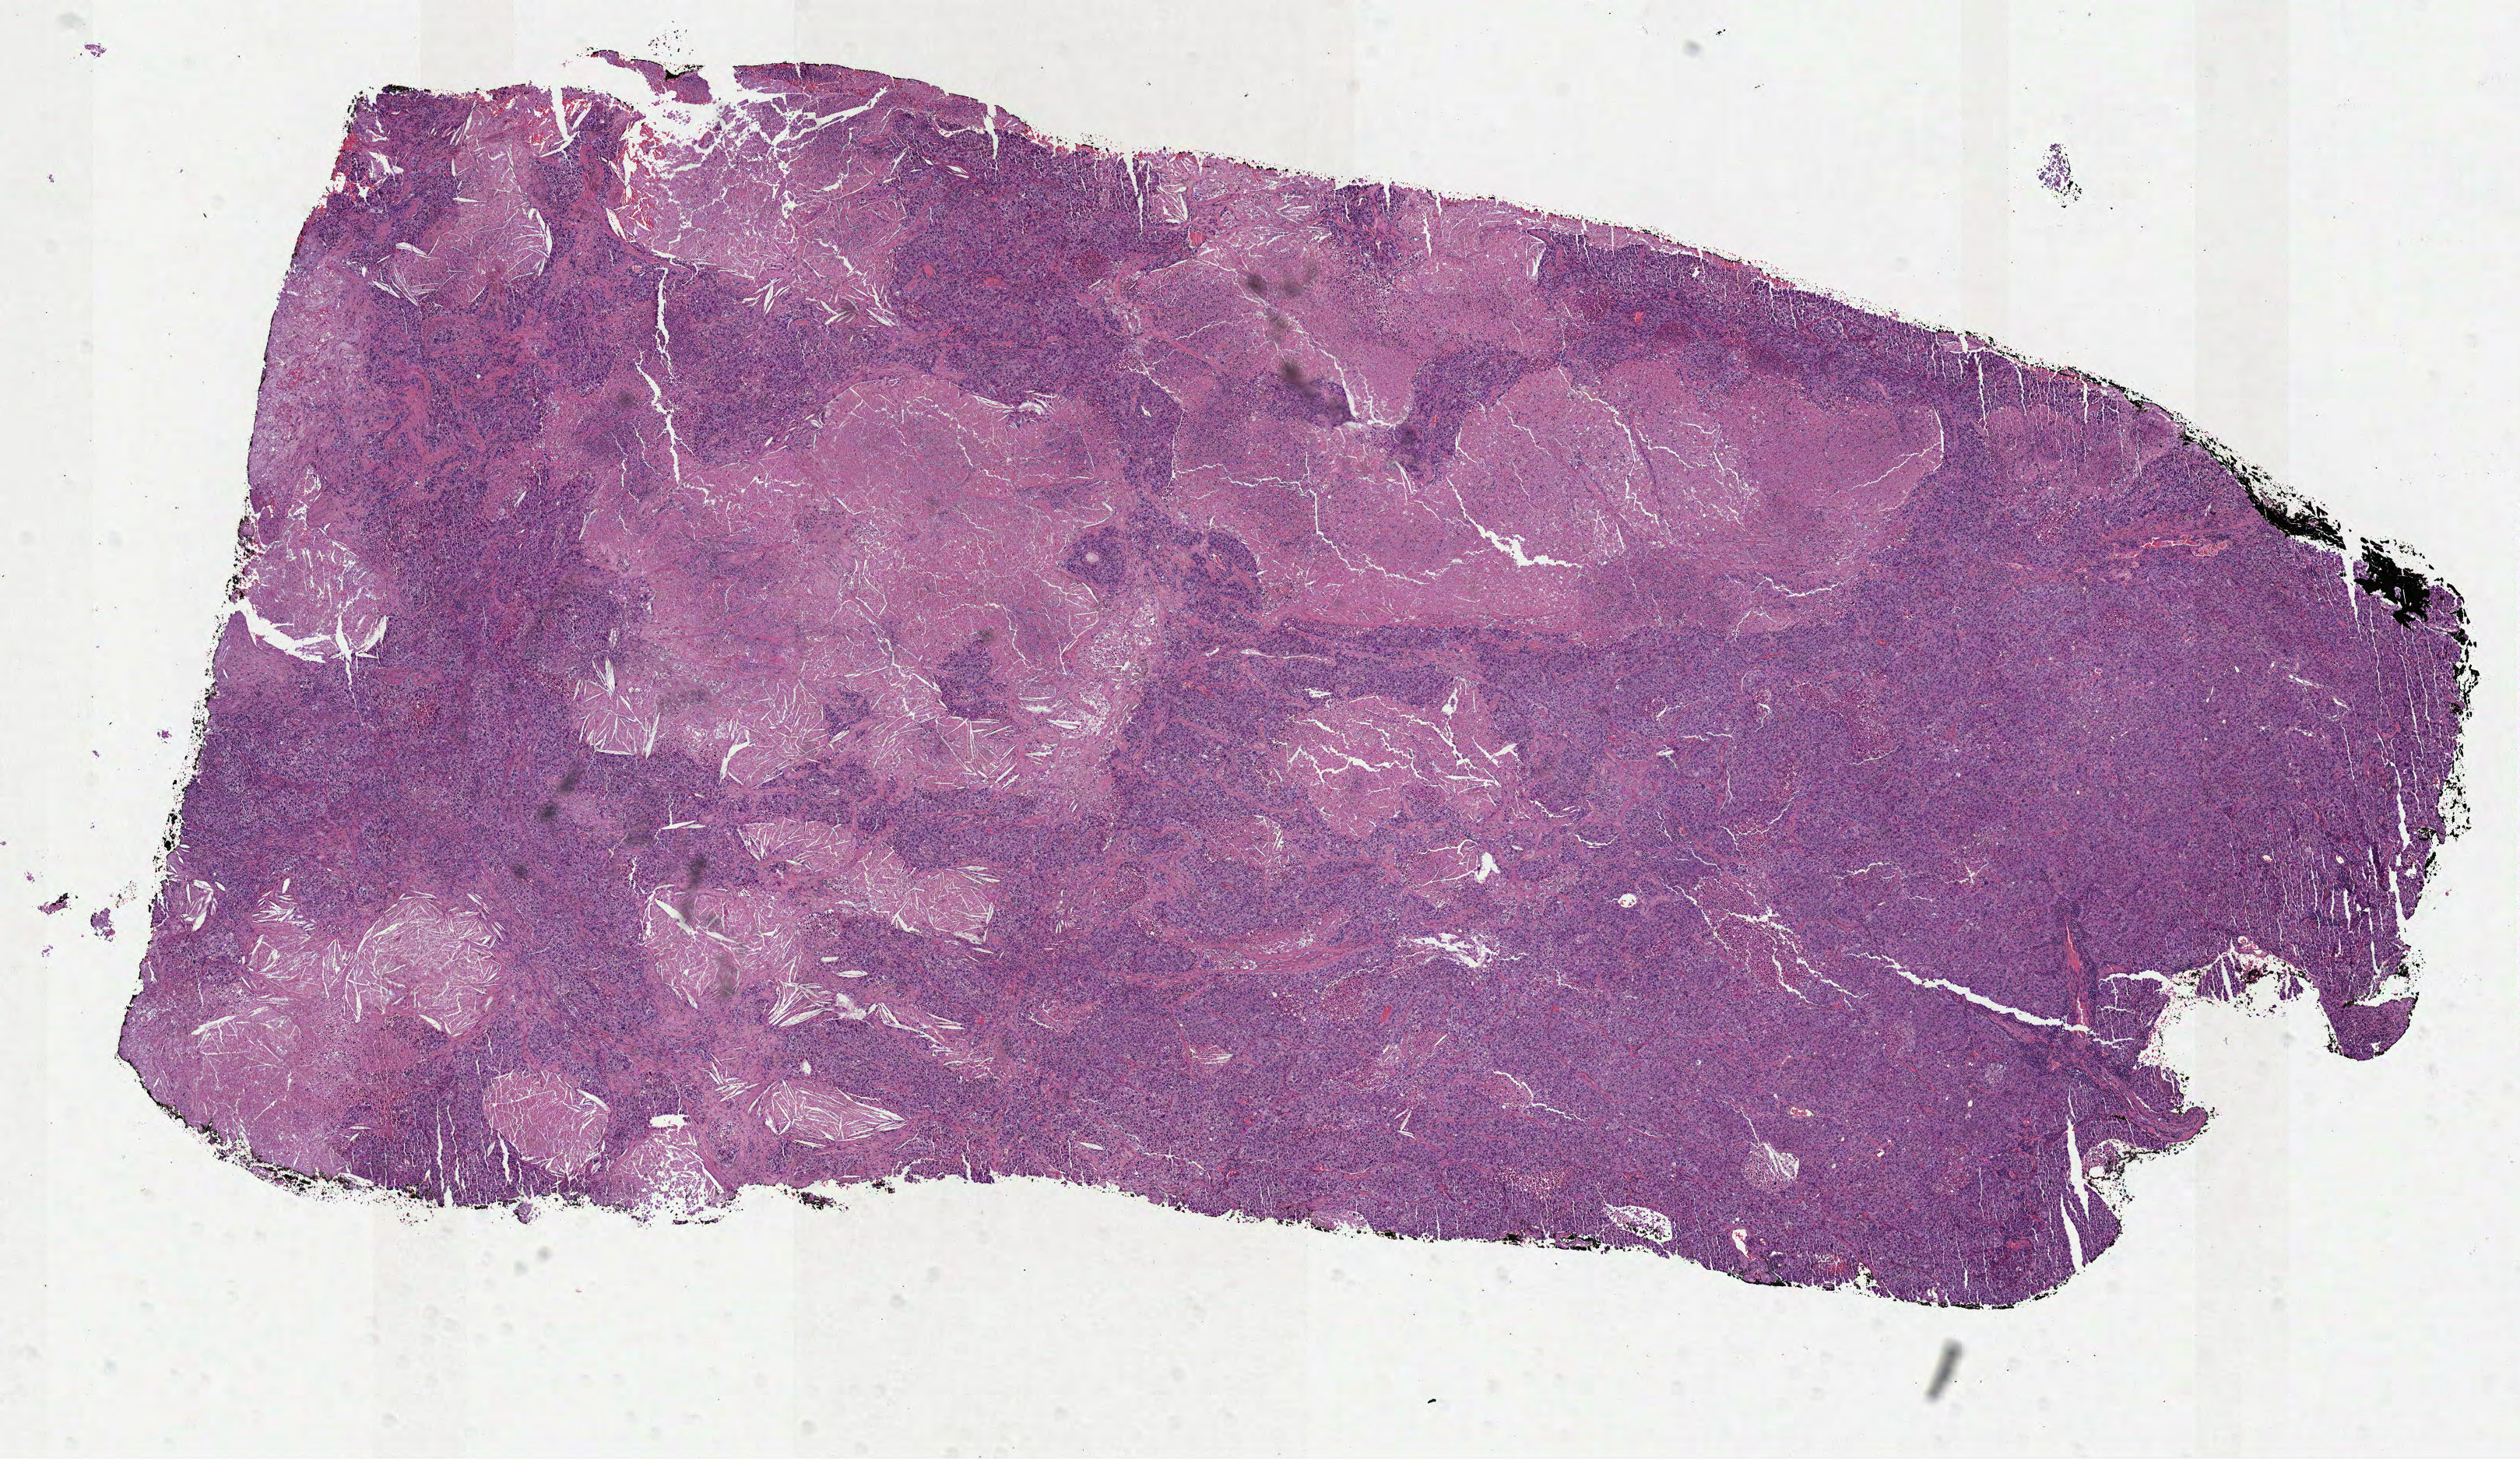
H&E whole-slide image — whole scanned area (about 13.1 x 7.6 mm) shown as a low-resolution overview; formalin-fixed paraffin-embedded (FFPE) diagnostic section; lung, primary tumour sample. Male patient; age at initial diagnosis 81 years.
Histologic diagnosis: Adenocarcinoma, NOS (upper lobe, lung). AJCC pathologic stage: IIB (7th edition). TNM: T3 N0 MX.